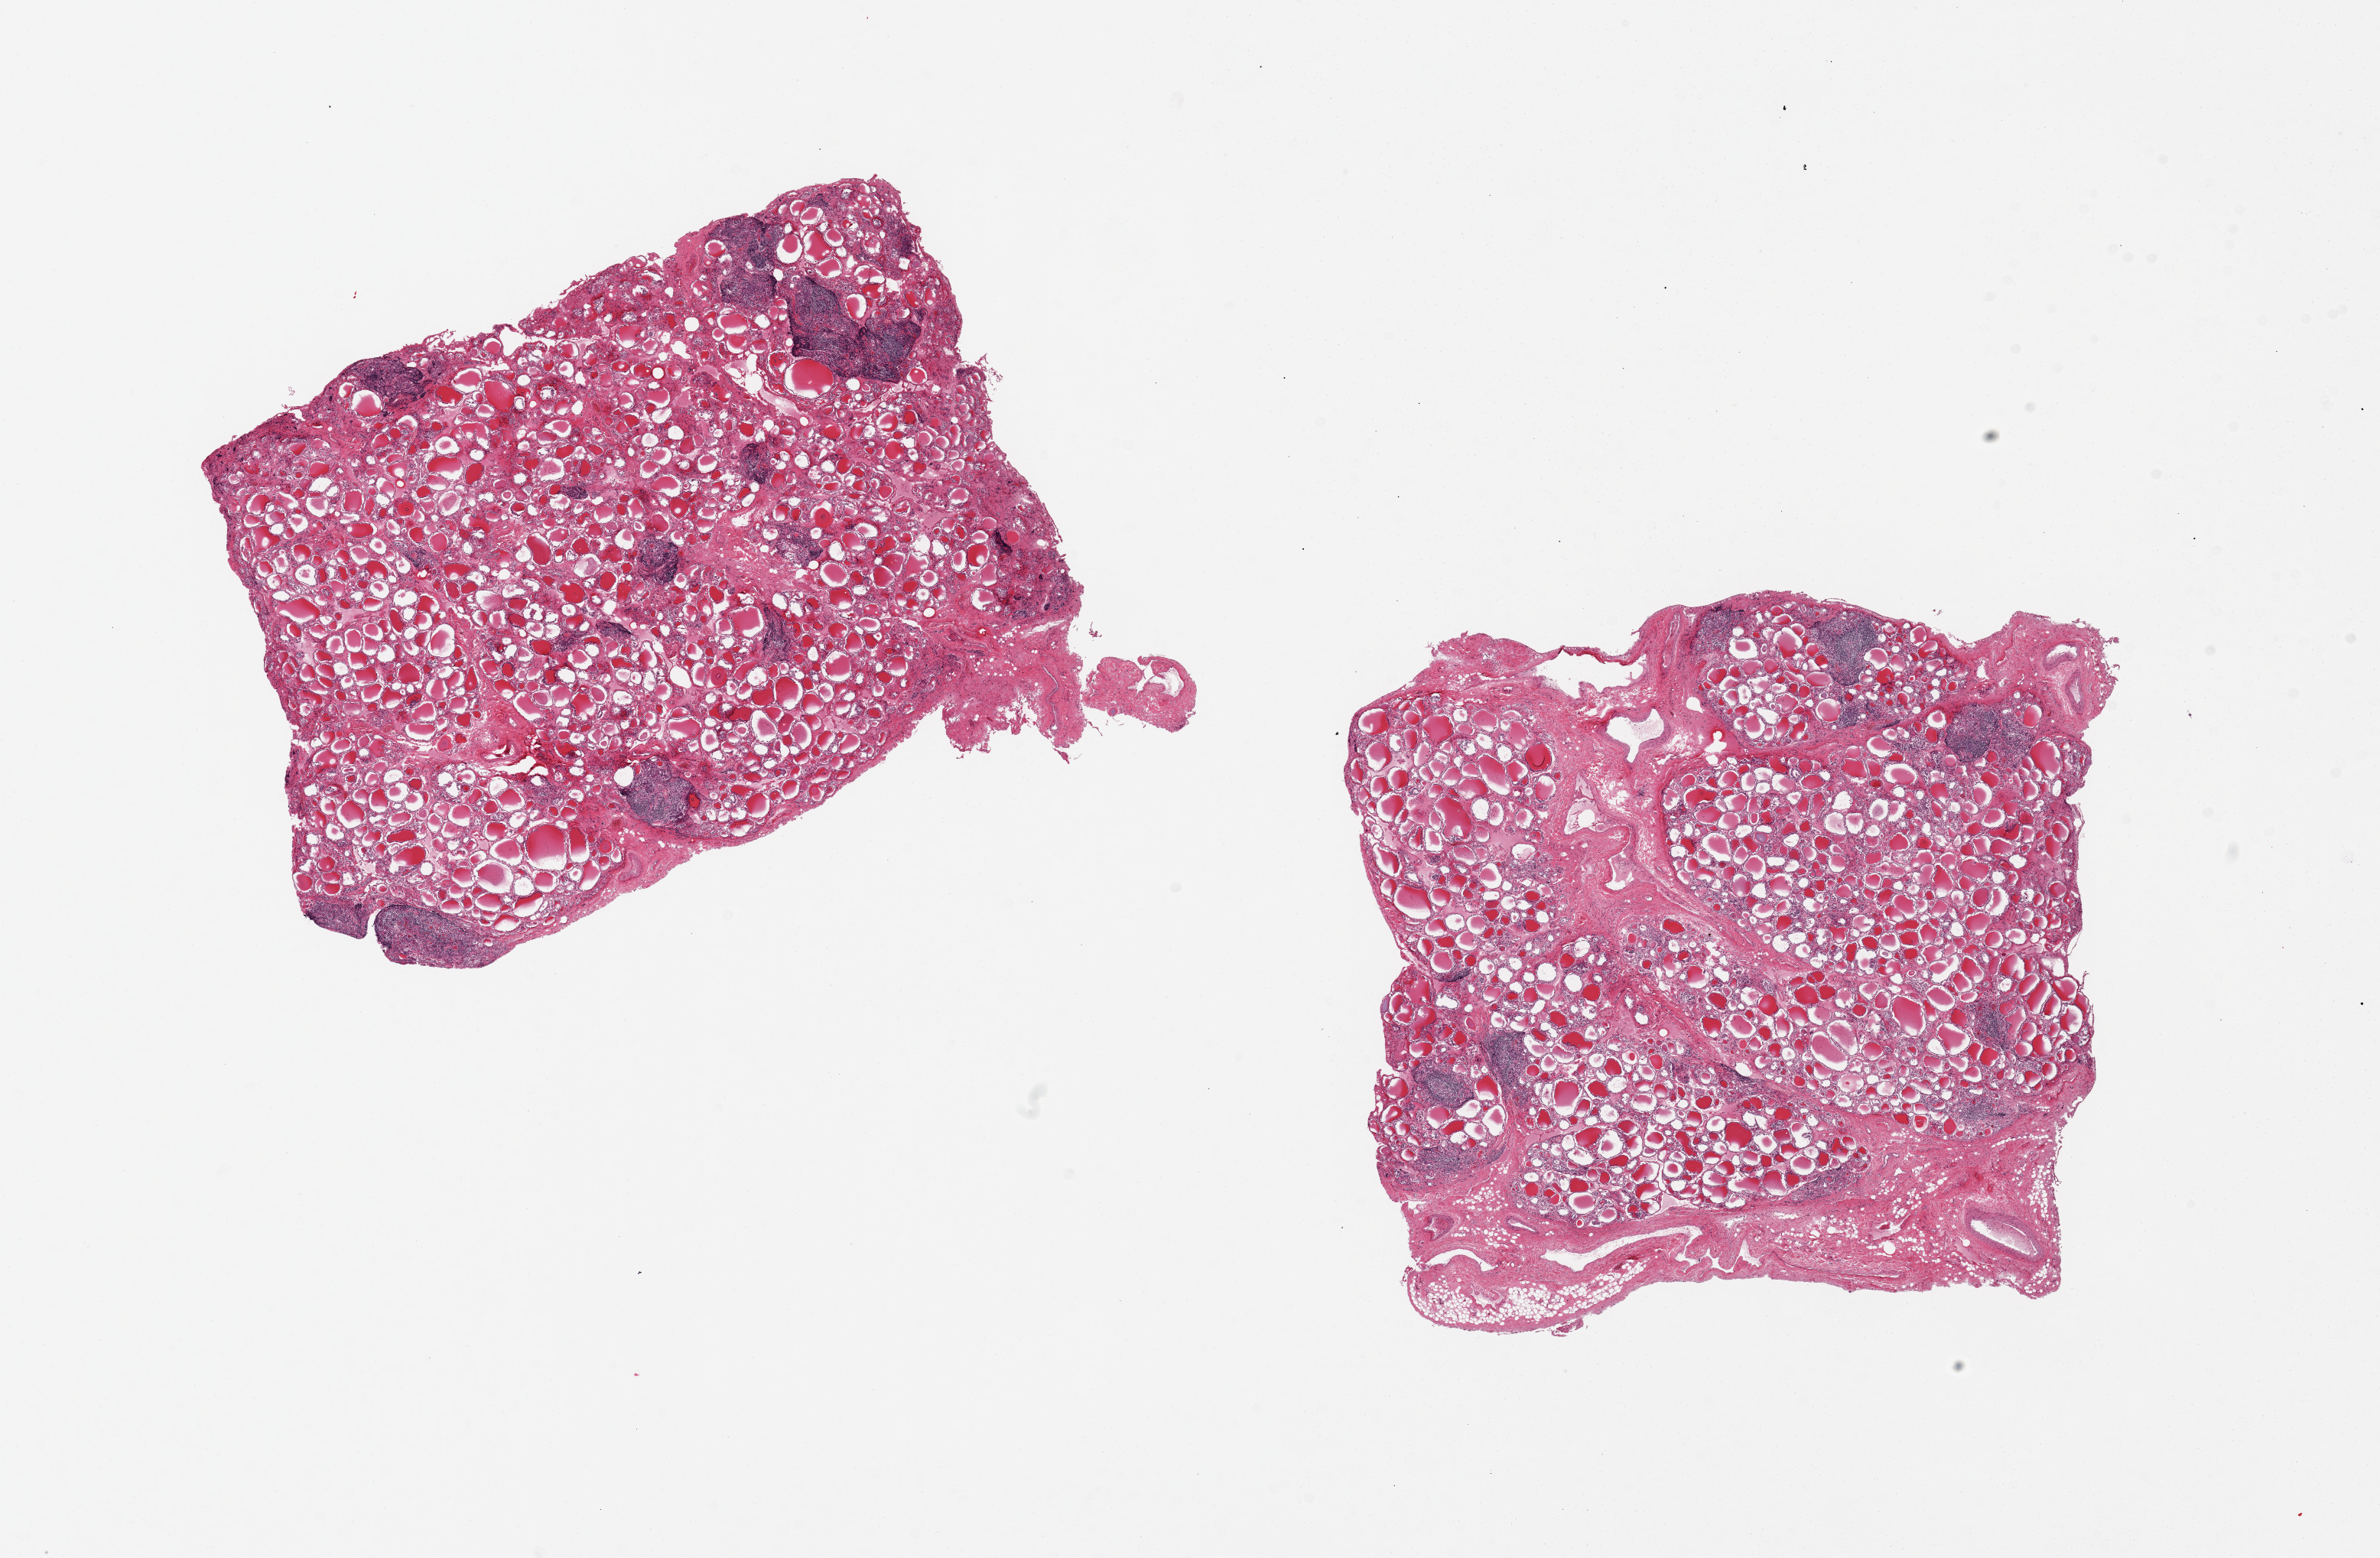
H&E whole-slide image, shown as a low-resolution overview of the whole scanned area (about 24.6 x 16.1 mm, from a 20x scan); PAXgene-fixed, paraffin-embedded tissue; section of thyroid (target tissue); tissue donor sample. Male donor.
Reviewer comment on this tissue sample: 2 pieces; patchy areas of lymphocytic or Hashimoto's thyroiditis.